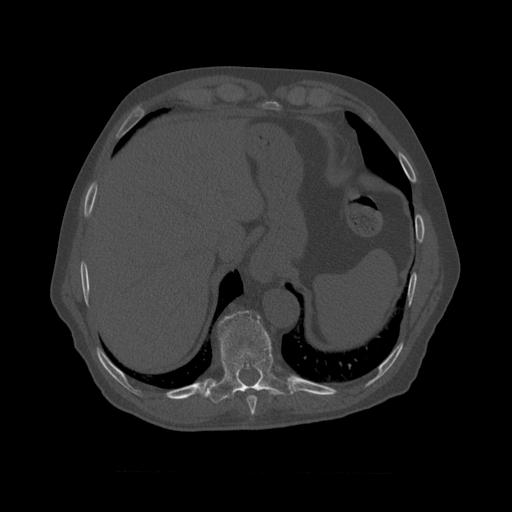
CT including the spine, one axial slice; slice 428 of 450 in the series (ordered by position); reconstruction kernel STANDARD; 120 kVp; bone window (W 1800 / L 400 HU); 1.25 mm slice thickness; 512 × 512 image matrix, field of view 405 × 405 mm. Patient age 75 years. Case-level facts recorded for this patient, not image findings: primary cancer: prostate.
Structures marked on this image (semi-automatic segmentation, software-assisted and operator-edited):
- T8 vertebra: box from (x=247, y=395) to (x=258, y=410) px
- T9 vertebra: (x=212, y=311)–(x=295, y=399)